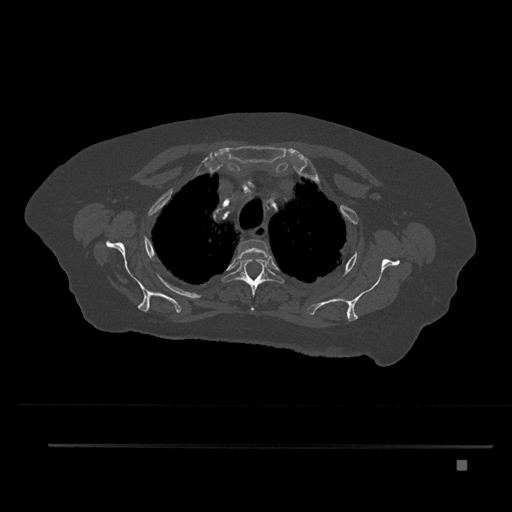
CT including the spine, one axial slice; reconstruction kernel Br40s/3; 120 kVp; bone window (W 1800 / L 400 HU); 512 × 512 image matrix, field of view 437 × 437 mm. Female patient, age 76 years. From the clinical record (not read from this slice): primary cancer: lung.
Structures marked on this image (semi-automatic segmentation, software-assisted and operator-edited):
- T2 vertebra: bounding box (x1, y1, x2, y2) in pixels: (238, 239, 270, 259)
- T3 vertebra: (222, 257, 285, 310)